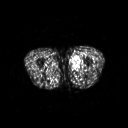
FDG PET of an extremity soft-tissue mass (from a PET/CT study), one axial slice. Slice 234 of 311 in the series (ordered by position). 3.27 mm slice thickness. 128 × 128 image matrix, field of view 500 × 500 mm. Male patient, age 29 years. From the clinical record (not read from this slice): histological type: mixoid liposarcoma; grade: low; site of the primary tumour: left thigh.
Structures marked on this image (expert contour drawn on MRI and transferred to this co-registered scan by the dataset authors):
- gross tumour volume (mass): bounding box <71,54,82,69> (left, top, right, bottom; pixels)